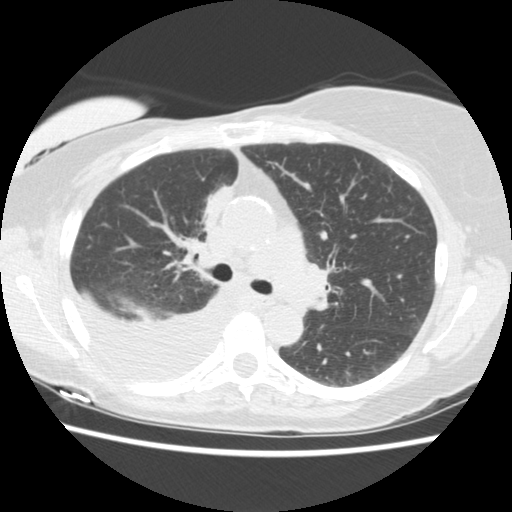
Low-dose screening chest CT, one axial slice; position 95 of 157 along the scan axis; lung window (W 1500 / L -600 HU); 2.5 mm slice thickness; 512 × 512 image matrix.
Outlined on this slice (expert manual segmentation):
- lesion 1 (tumor, upper lobe of right lung): bounding box (x1, y1, x2, y2) in pixels: (205, 187, 233, 224)